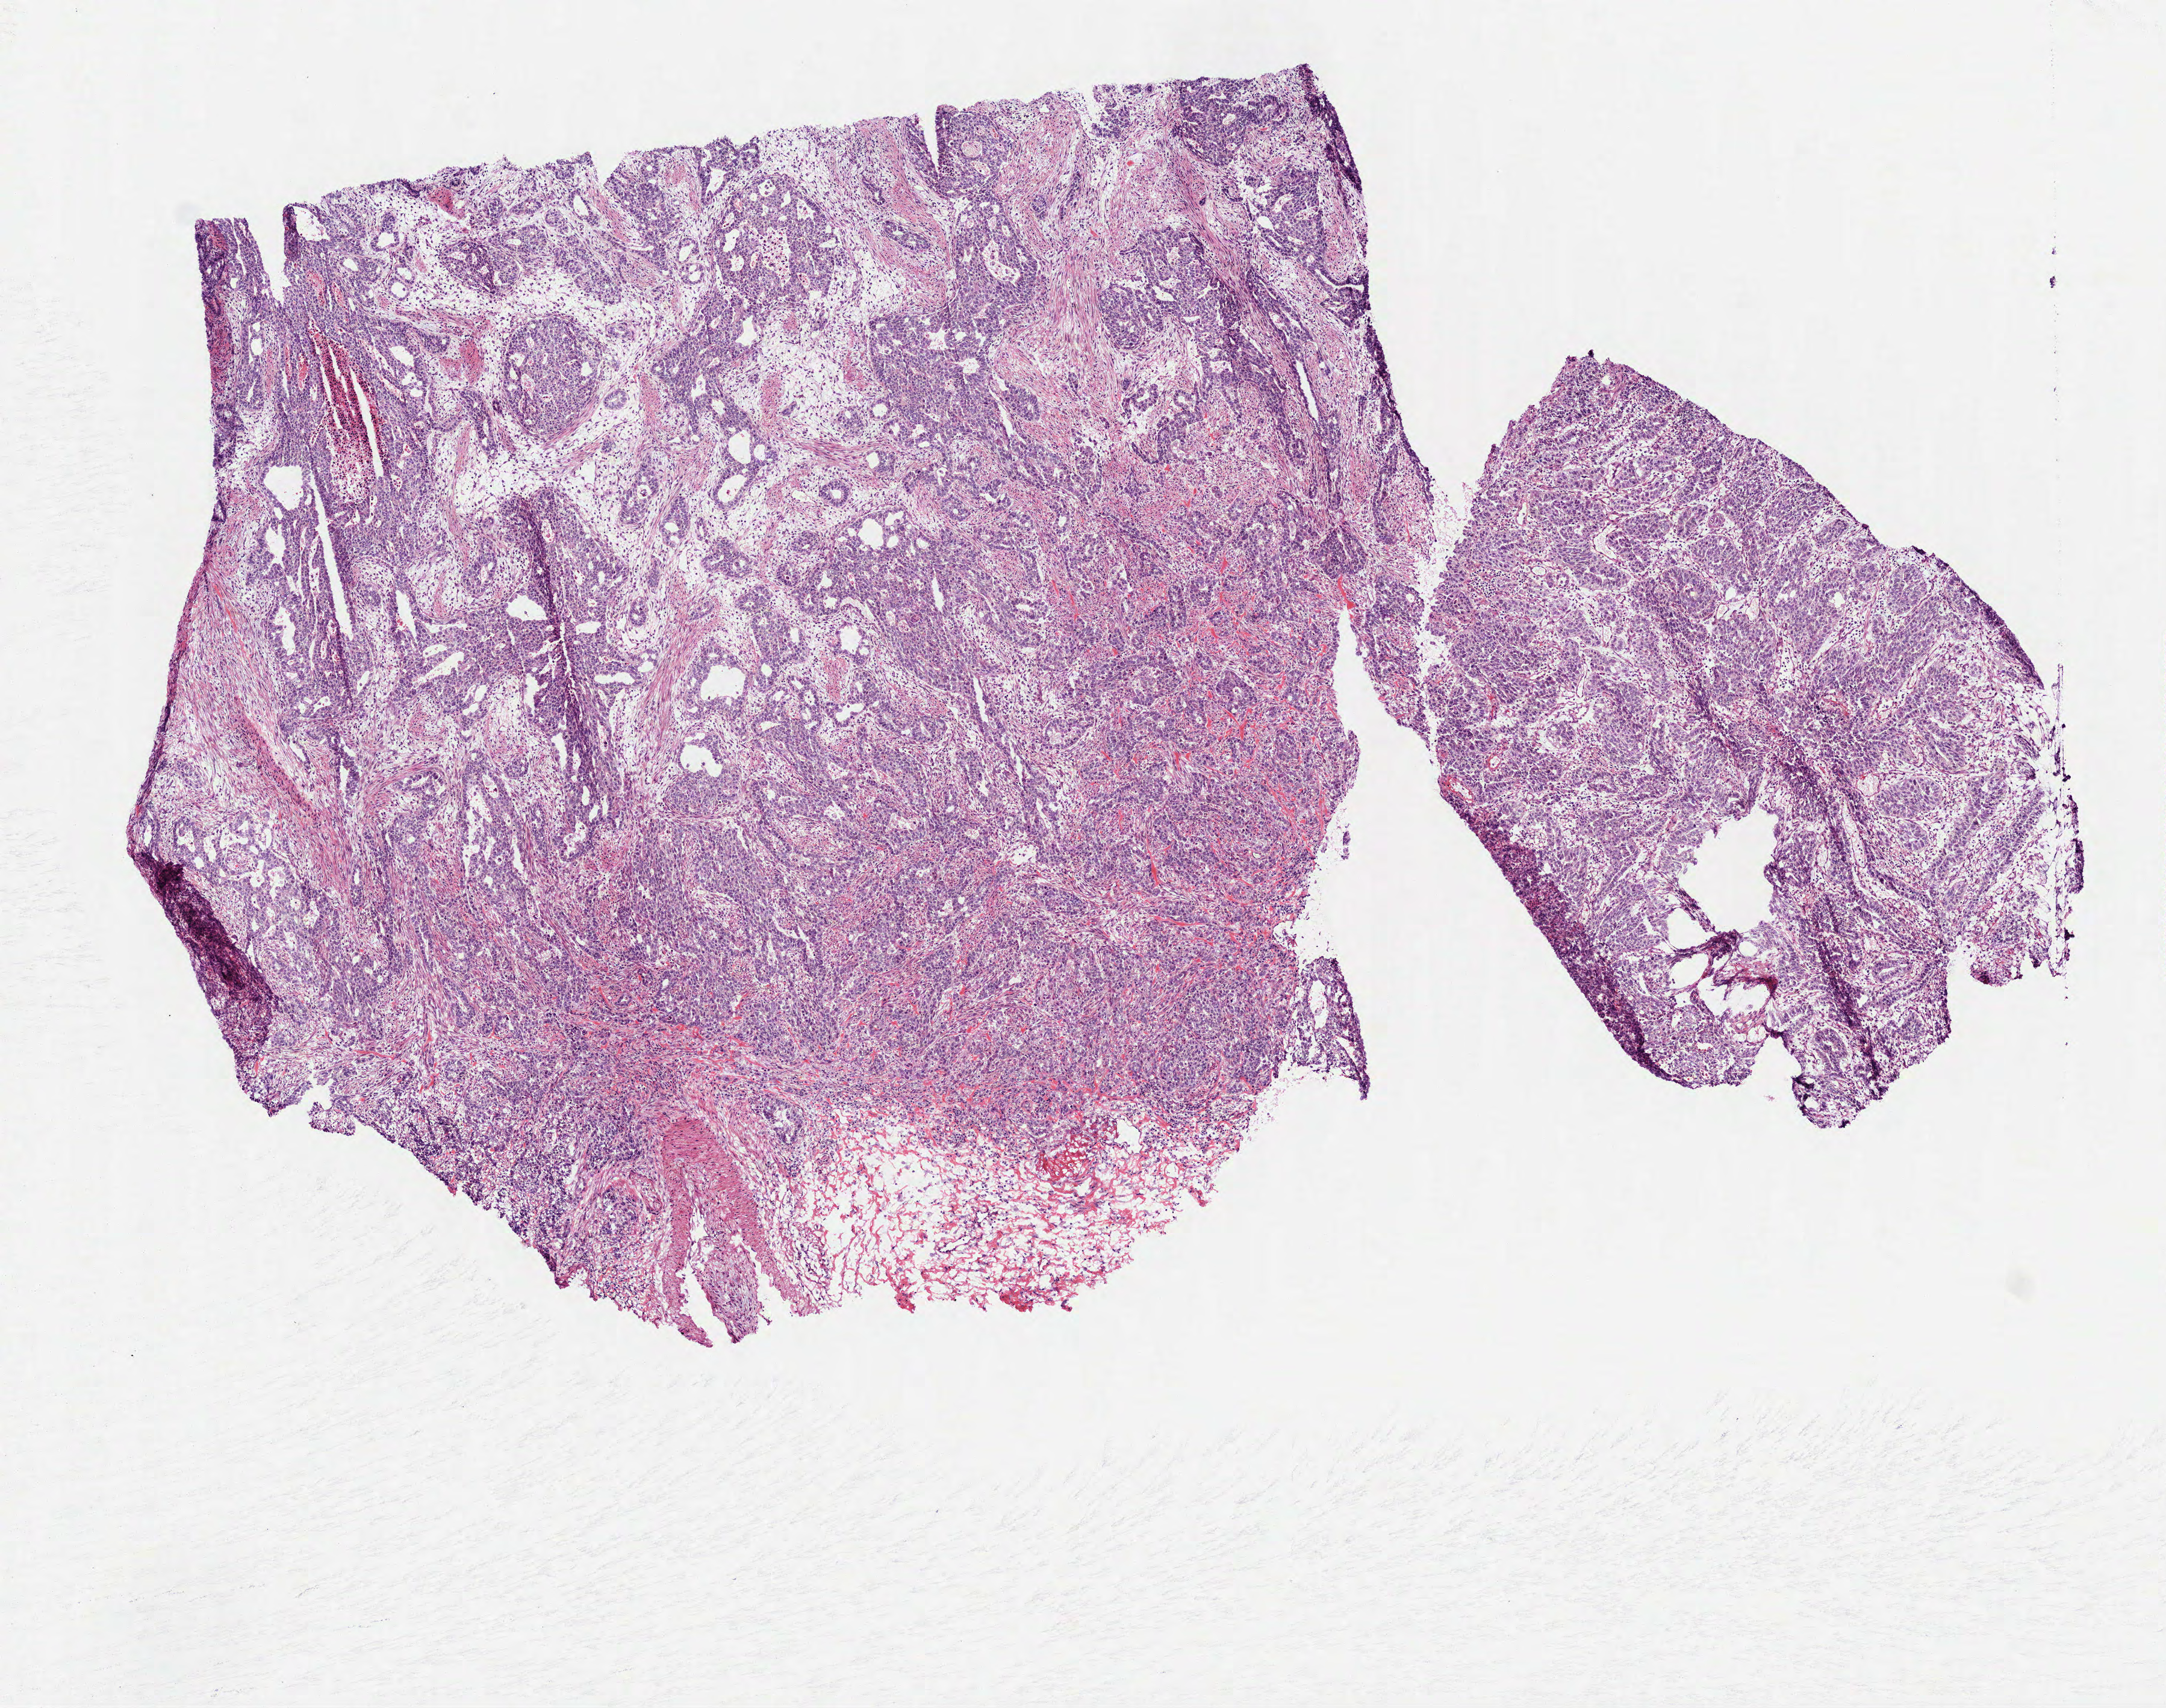
H&E-stained whole-slide image — a low-resolution overview of the entire scanned area, about 7.3 x 5.7 mm (acquisition: 40x scan). Frozen section from the top of the tissue portion. Stomach, primary tumour sample. Patient sex: male. Histologic grade: G2 (moderately differentiated). Composition of this section per pathologist review: tumour cells 98%, tumour nuclei 70%, normal cells 0%, stromal cells 0%, necrosis 2%. Infiltration values recorded for this section: lymphocyte infiltration 10%, monocyte infiltration 2%, neutrophil infiltration 7%.
AJCC pathologic stage: IIIA (6th edition). Lymph nodes positive (case pathology): 2 of 12 examined. Diagnosis: Adenocarcinoma, NOS.